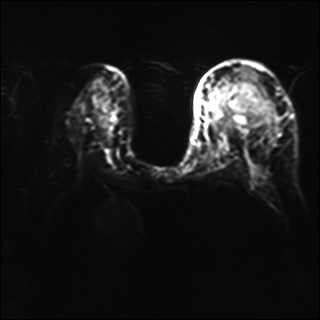
Breast MRI, one axial slice. Slice 21 of 40 in the series (ordered by position). Diffusion-weighted series; image 2 of 4 stored at this slice position (different b-values; order by instance number). 1.5 T. 4 mm slice thickness. 320 × 320 image matrix, field of view 320 × 320 mm. Female patient.
Annotated regions visible in this slice (expert manual segmentation):
- tumour on diffusion-weighted imaging: bounding box (x1, y1, x2, y2) in pixels: (234, 82, 263, 122)